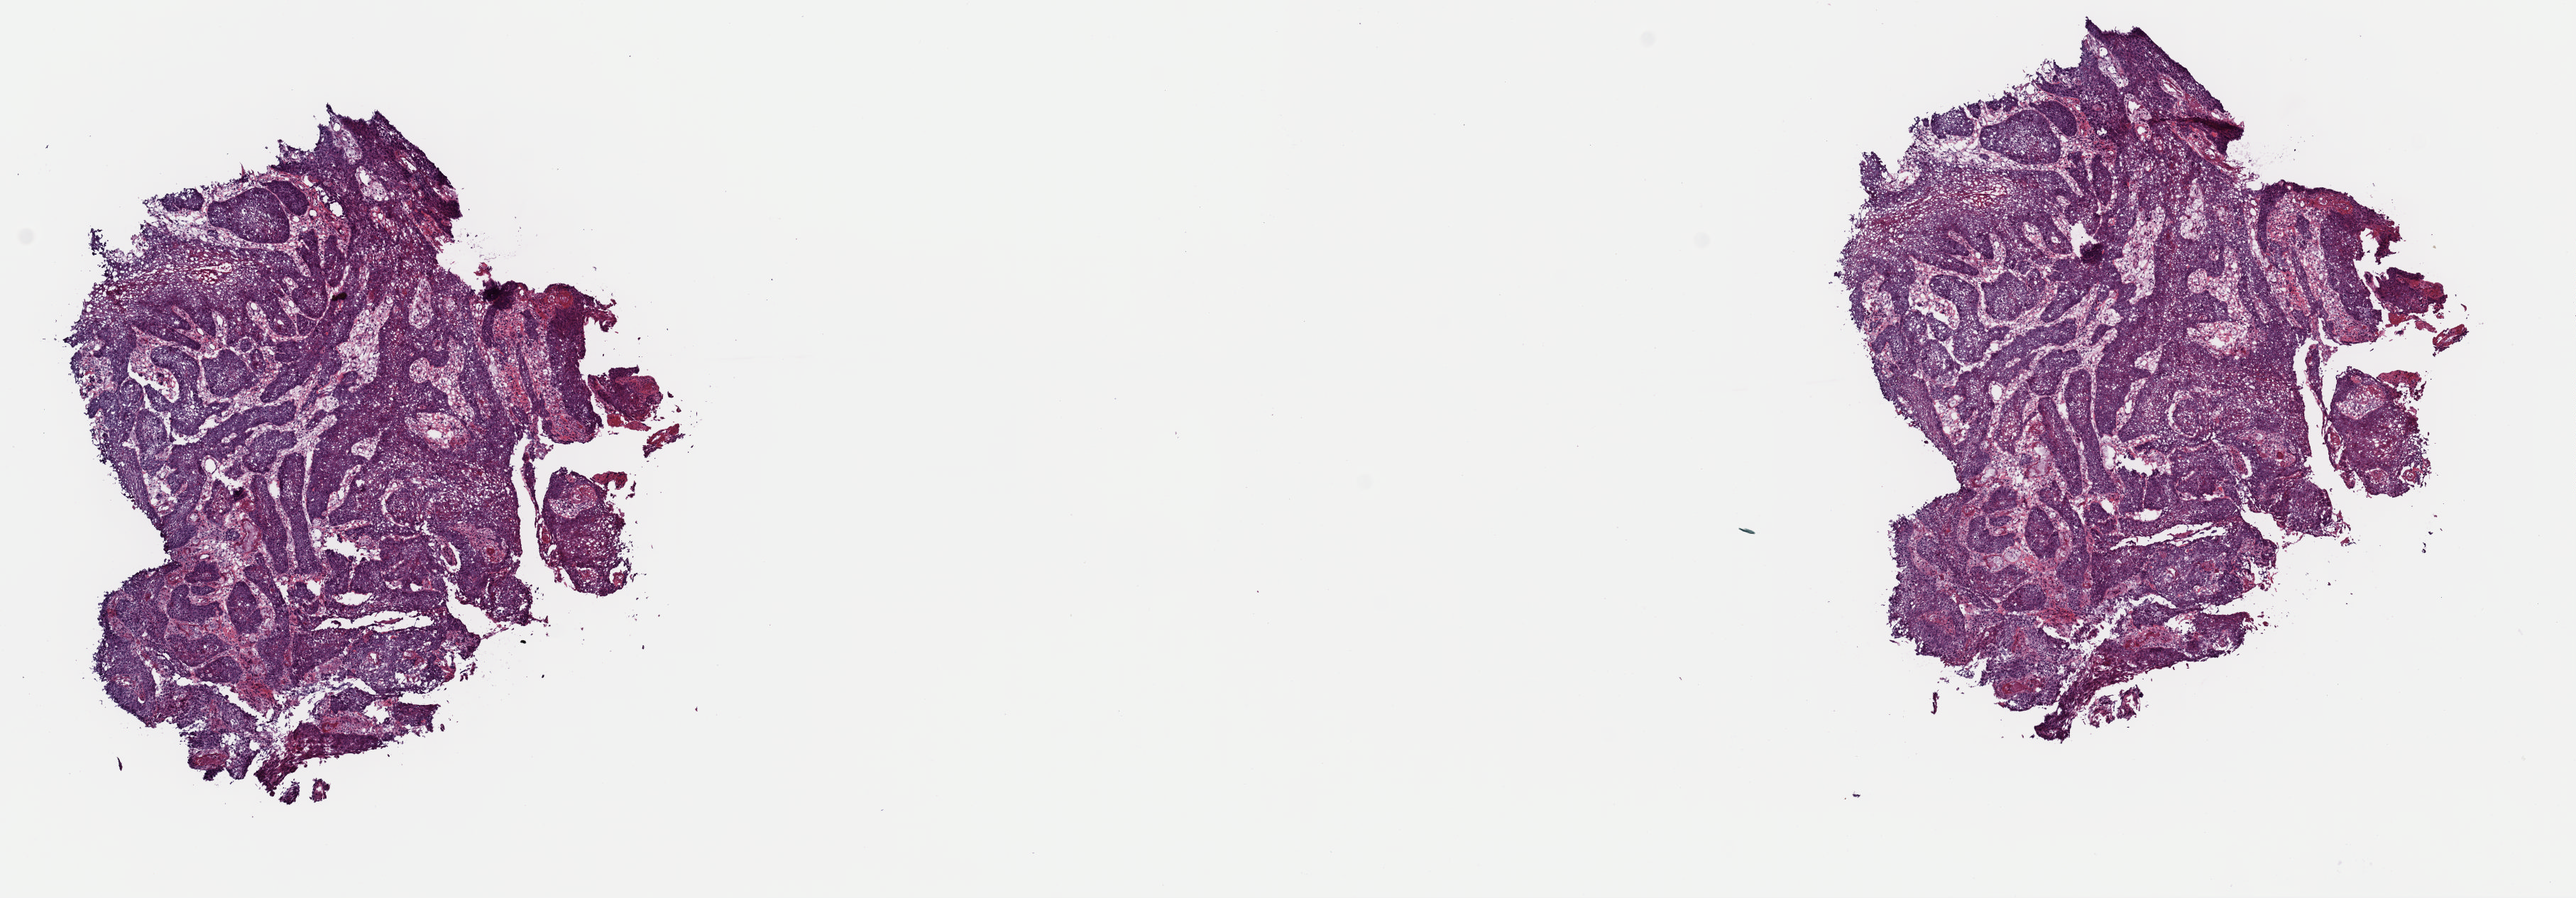
H&E-stained whole-slide image, shown as a low-resolution overview of the whole scanned area (about 14.3 x 5.0 mm, slide scanned at 40x). Frozen section from the top of the tissue portion. Primary tumour sample from the head and neck. Patient: male, age at initial diagnosis 57 years. Histologic grade: G2 (moderately differentiated). Slide review estimates, as recorded: tumour cells 80%, tumour nuclei 95%, normal cells 0%, stromal cells 20%, necrosis 0%. Infiltration values recorded for this section: lymphocyte infiltration 3%, monocyte infiltration 1%, neutrophil infiltration 0%.
Pathologic diagnosis: Squamous cell carcinoma, keratinizing, NOS (floor of mouth, NOS). AJCC pathologic stage: IVA (7th edition). Lymph nodes positive (case pathology): 5 of 39 examined.